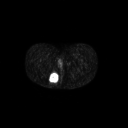
FDG PET of an extremity soft-tissue mass (from a PET/CT study), one axial slice. Position 24 of 267 along the scan axis. 128 × 128 image matrix, field of view 700 × 700 mm. Female patient, age 17 years. From the clinical record (not read from this slice): histological type: epithelioid sarcoma; grade: intermediate; site of the primary tumour: right buttock.
Annotated regions visible in this slice (expert contour drawn on MRI and transferred to this co-registered scan by the dataset authors):
- gross tumour volume including surrounding oedema: bounding box <48,72,59,84> (left, top, right, bottom; pixels)
- gross tumour volume (mass): <49,73,59,83>